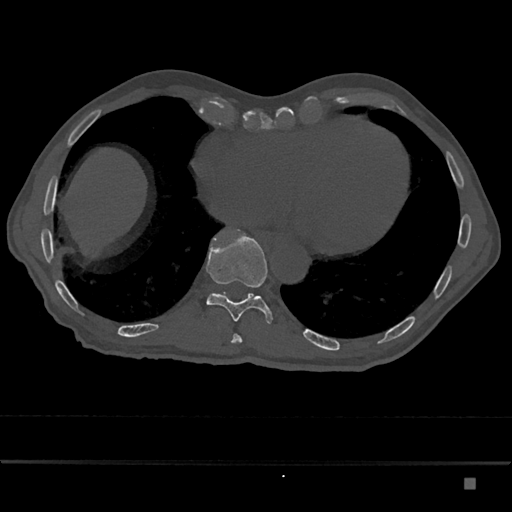
CT including the spine, one axial slice; position 738 of 797 along the scan axis; reconstruction kernel Br40s/3; 120 kVp; bone window (W 1800 / L 400 HU); 0.5 mm slice thickness; 512 × 512 image matrix, field of view 390 × 390 mm. Patient: male, 72 years. From the clinical record (not read from this slice): primary cancer: prostate.
Outlined on this slice (semi-automatically segmented with operator editing):
- T10 vertebra: box from (x=206, y=230) to (x=272, y=323) px
- T9 vertebra: (x=232, y=334)–(x=242, y=343)